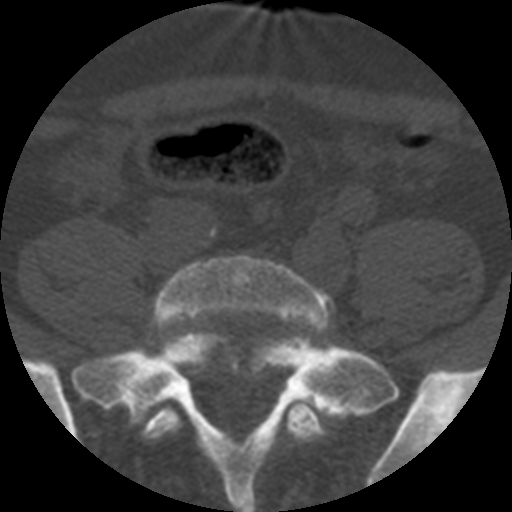
CT including the spine, one axial slice. Position 51 of 508 along the scan axis. Reconstruction kernel STANDARD. 120 kVp. Bone window (W 1800 / L 400 HU). 1.25 mm slice thickness. 512 × 512 image matrix, field of view 160 × 160 mm. Patient age 57 years. Case-level facts recorded for this patient, not image findings: primary cancer: prostate.
Annotated regions visible in this slice (semi-automatically segmented with operator editing):
- L5 vertebra: box from (x=137, y=254) to (x=334, y=442) px